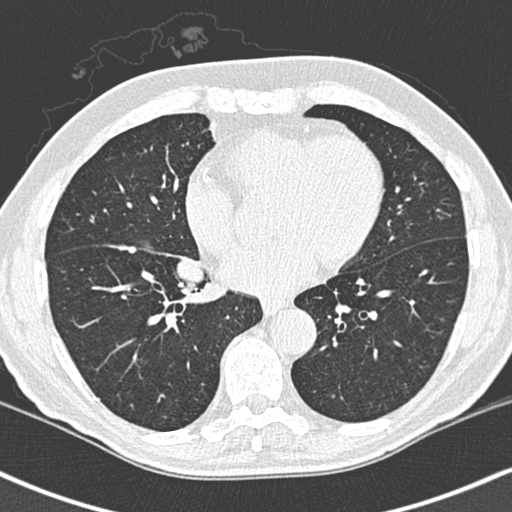
Low-dose screening chest CT, one axial slice. Slice 111 of 248 in the series (ordered by position). Lung window (W 1500 / L -600 HU). 1.3 mm slice thickness. 512 × 512 image matrix.
Annotated regions visible in this slice (expert manual segmentation):
- lesion 1 (tumor, lower lobe of right lung): box from (x=107, y=207) to (x=137, y=216) px